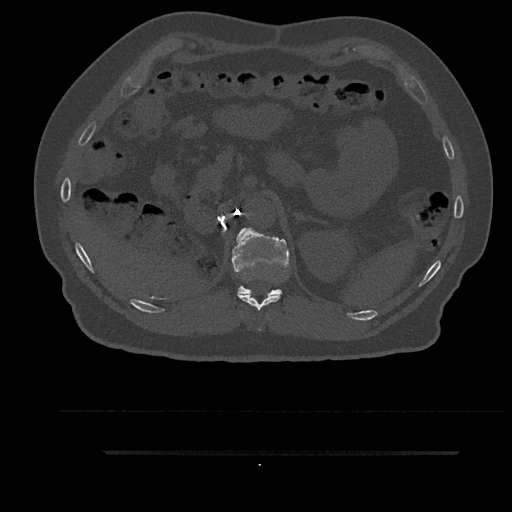
CT including the spine, one axial slice; slice 272 of 797 in the series (ordered by position); 120 kVp; bone window (W 1800 / L 400 HU); 512 × 512 image matrix. Male patient, age 63 years. From the clinical record (not read from this slice): primary cancer: renal; vertebrae with lytic lesions (as recorded): T8.
Outlined on this slice (semi-automatic segmentation, software-assisted and operator-edited):
- T11 vertebra: bounding box (x1, y1, x2, y2) in pixels: (238, 294, 282, 331)
- T12 vertebra: (232, 228, 289, 296)